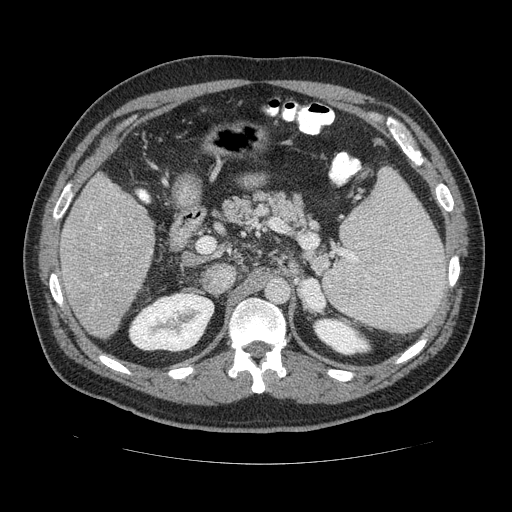
Contrast-enhanced abdominal CT (liver protocol), one axial slice; position 70 of 113 along the scan axis; 120 kVp; soft-tissue window (W 400 / L 40 HU); 2.5 mm slice thickness; 512 × 512 image matrix. Case-level facts recorded for this patient, not image findings: diagnosis: hepatocellular carcinoma (patient treated with transarterial chemoembolisation; whether this scan precedes or follows treatment is not stated here); TNM stage (as recorded): Stage-II; Child-Pugh class: B; tumour differentiation: moderately differentiated; tumour nodularity: multinodular.
Structures marked on this image (semi-automatic segmentation, software-assisted and operator-edited):
- liver parenchyma outside the tumour (the mass and vessels are separate outlines, so this box may not span the whole liver): bounding box (x1, y1, x2, y2) in pixels: (58, 170, 156, 340)
- liver vessels: (99, 224, 153, 276)